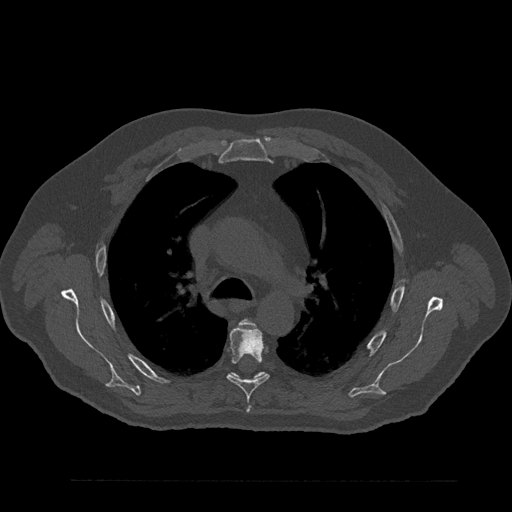
CT including the spine, one axial slice; position 599 of 797 along the scan axis; 120 kVp; bone window (W 1800 / L 400 HU); 0.5 mm slice thickness; 512 × 512 image matrix, field of view 430 × 430 mm. Male patient, age 61 years. Case-level facts recorded for this patient, not image findings: primary cancer: prostate.
Annotated regions visible in this slice (semi-automatic segmentation, software-assisted and operator-edited):
- T4 vertebra: bounding box [x1, y1, x2, y2] px = [241, 320, 253, 325]
- T5 vertebra: [227, 326, 269, 408]
- T6 vertebra: [229, 372, 266, 381]